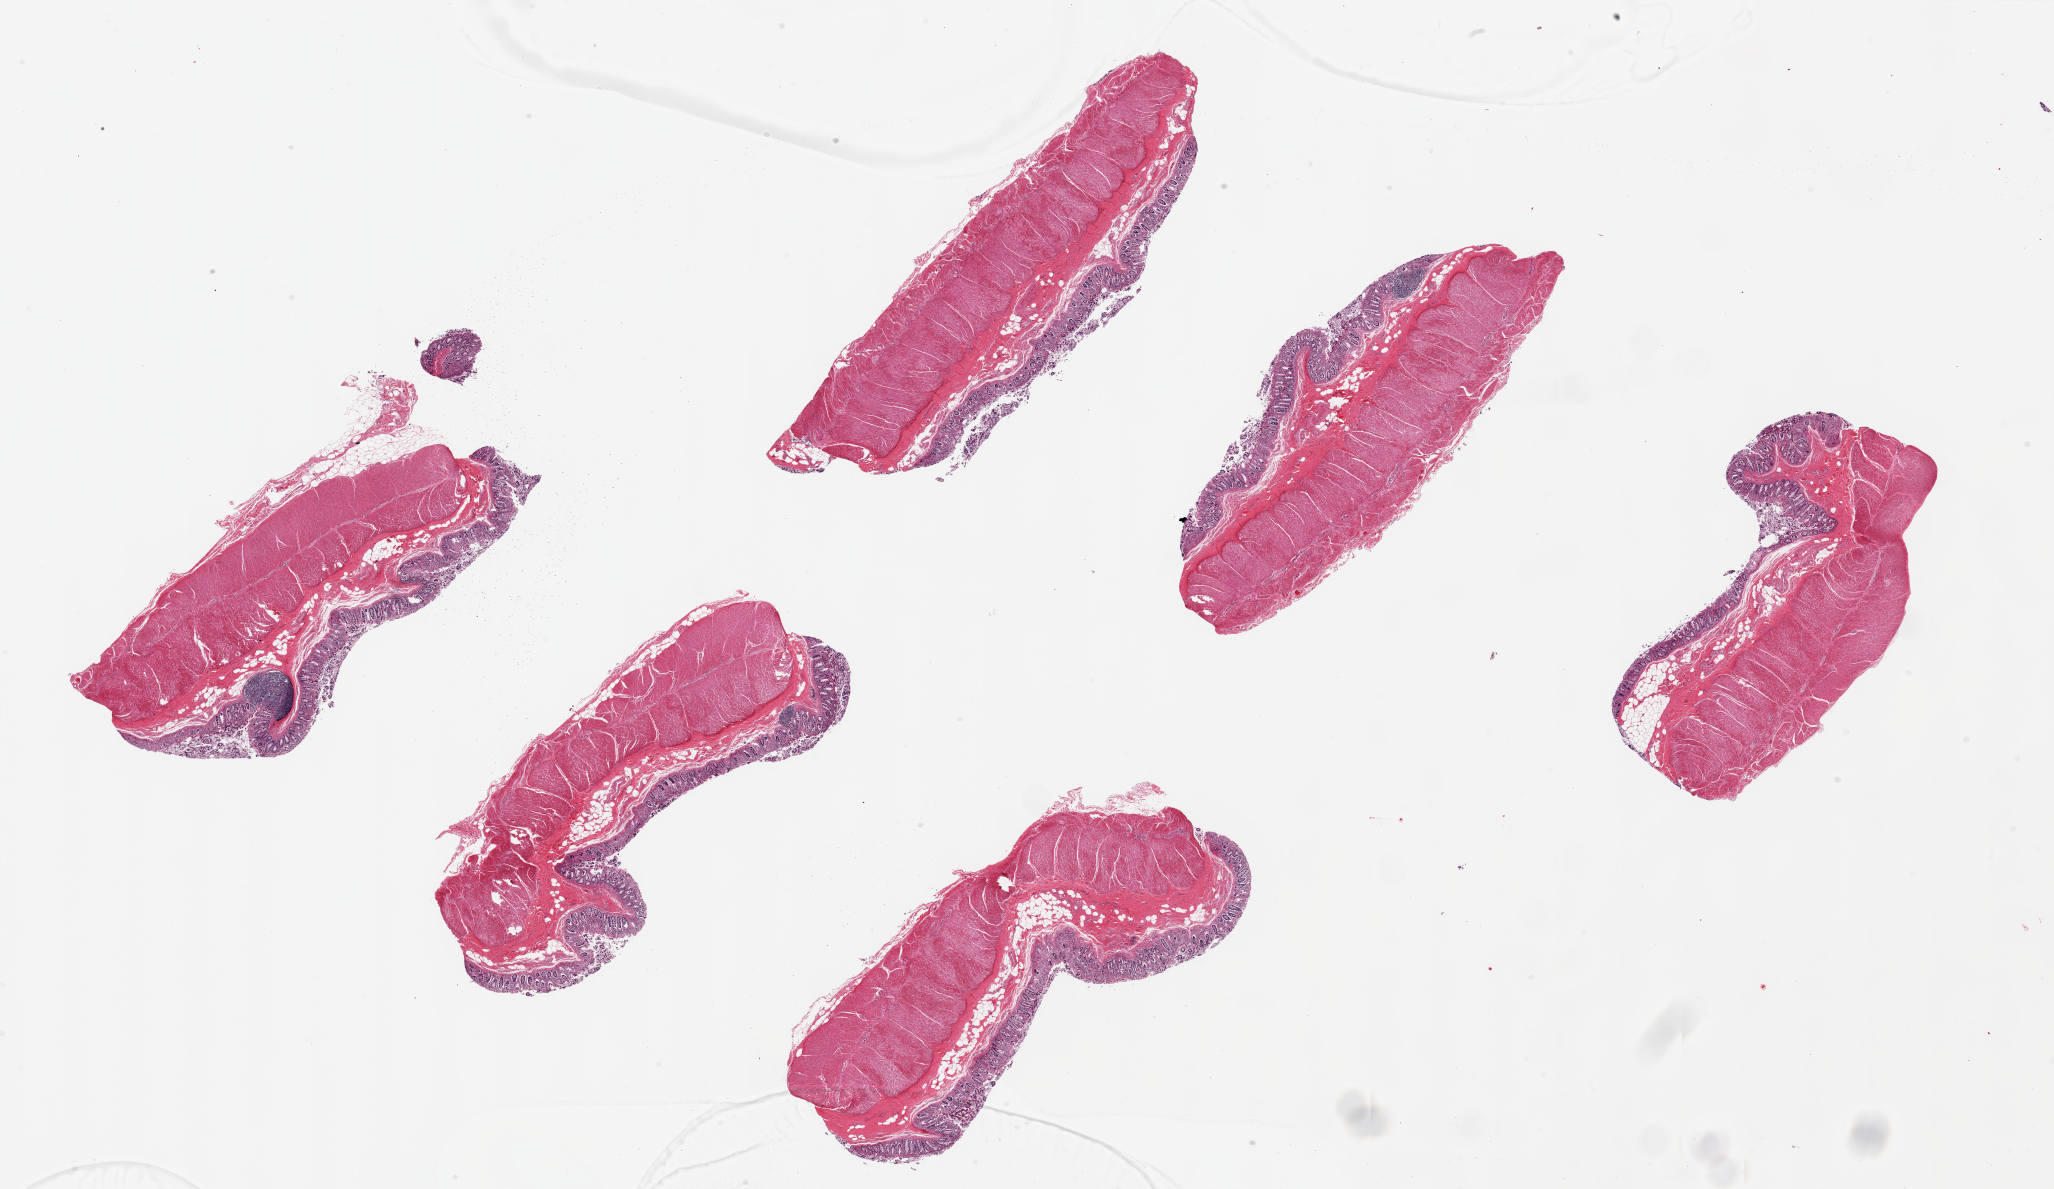
Digitized H&E-stained section — whole scanned area (about 32.5 x 18.8 mm) shown as a low-resolution overview; PAXgene-fixed, paraffin-embedded tissue; section of transverse colon (target tissue); tissue donor sample. Donor: female.
- review note (as recorded): 6 pieces, ~6.5x2.5. Mucosa moderately autolyzed, ~ 10--15% of thickness